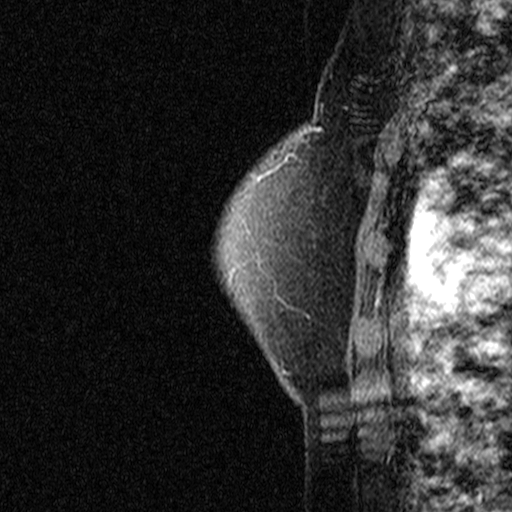
Breast MRI (dynamic contrast-enhanced), one sagittal slice; position 34 of 44 along the scan axis; dynamic contrast-enhanced study with each time point stored as its own series, time point 2 of 3 at this slice position (early post-contrast, ordered by acquisition time); 1.5 T; TE 4.5 ms, TR 11 ms; 3 mm slice thickness; 512 × 512 image matrix, field of view 200 × 200 mm. Female patient, age 49 years. From the clinical record (not read from this slice): setting: breast cancer imaged before/during neoadjuvant chemotherapy; receptor status: triple-negative.
Annotated regions visible in this slice (semi-automatically segmented with operator editing):
- analysis volume of interest (the breast-tissue region the enhancement analysis was run in; not a lesion): box from (x=276, y=94) to (x=369, y=181) px
- tumour enhancement mask (voxels above the 90 % enhancement threshold inside the analysis volume of interest): (x=318, y=129)–(x=323, y=131)